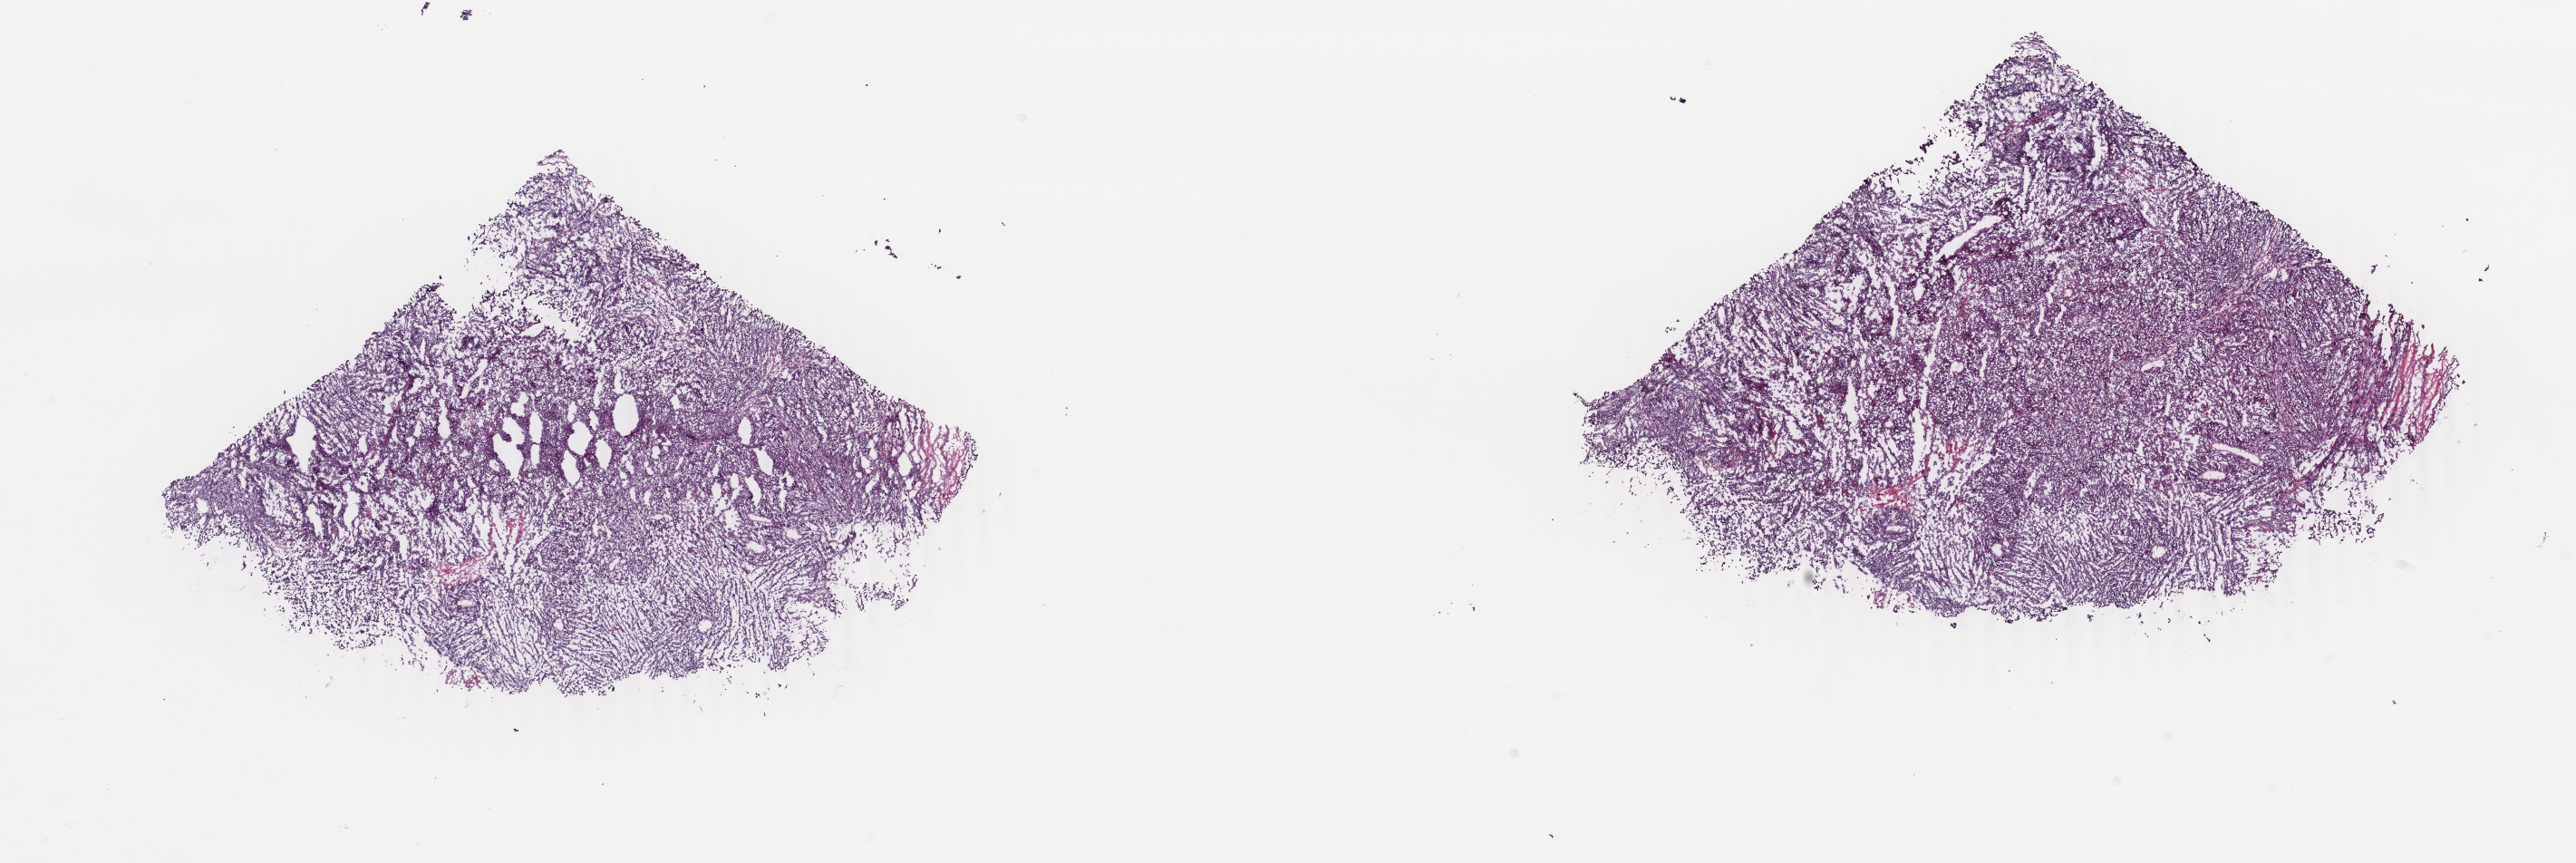
Whole-slide histology image, Hematoxylin and eosin (H&E) stained — a low-resolution overview of the entire scanned area, about 22.6 x 7.6 mm, frozen section from the top of the tissue portion, metastatic tumour sample. Female, age 75 years at initial diagnosis. Slide review estimates, as recorded: tumour cells 80%, tumour nuclei 85%, normal cells 0%, stromal cells 15%, necrosis 5%. Infiltration values recorded for this section: lymphocyte infiltration 5%, monocyte infiltration 0%, neutrophil infiltration 0%.
This section: metastatic tumour tissue. Patient diagnosis: Malignant melanoma, NOS.